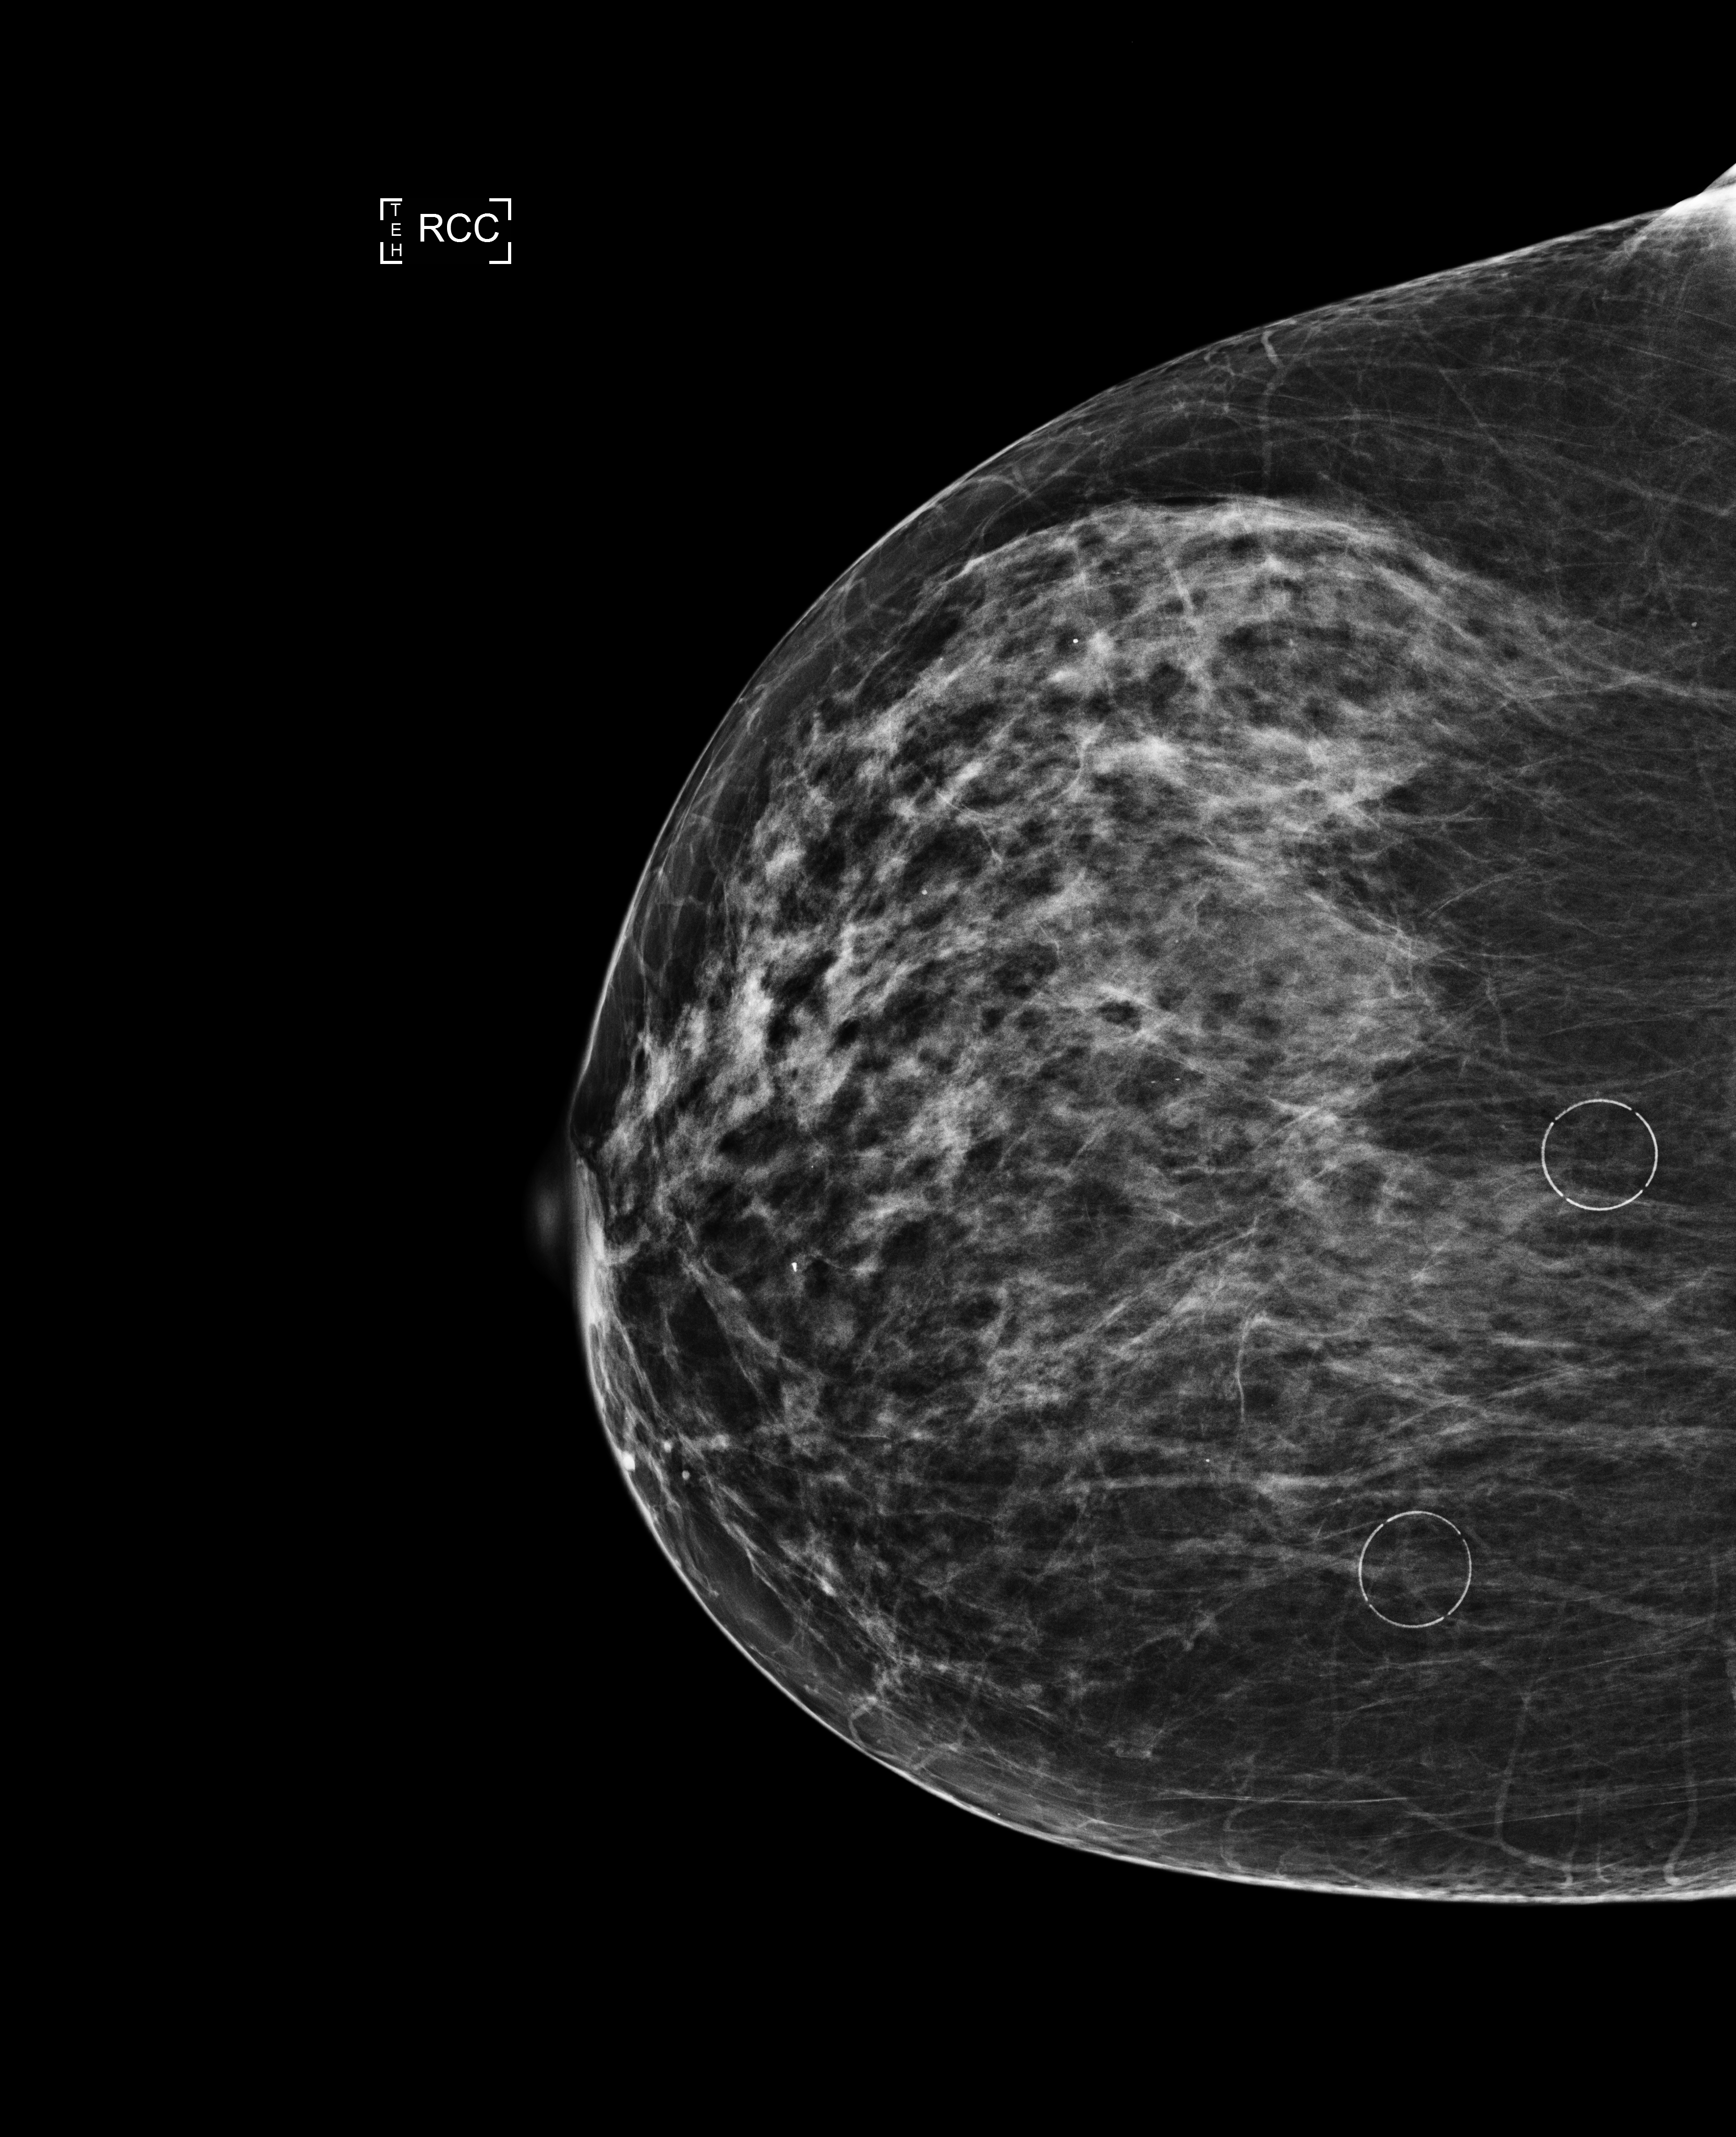
Full-field digital mammogram (FFDM), right breast, cranio-caudal projection, annual screening mammography examination. Female patient, age 61 years.
Breast density at the screening exam (both breasts): heterogeneously dense (BI-RADS density category c). Final BI-RADS category for the screening round (tomosynthesis exam, both breasts): category 2. Recall: recalled for additional imaging after this screen.